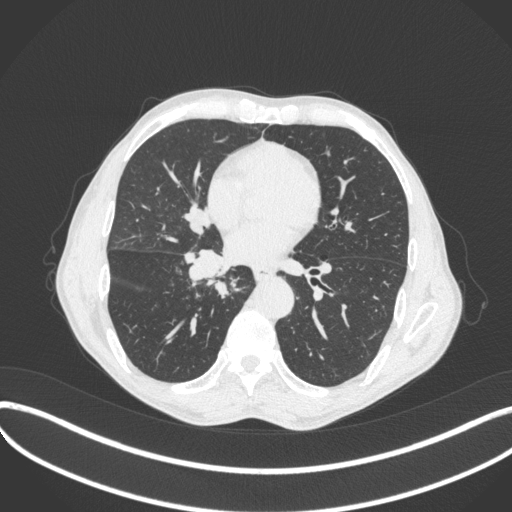
Chest CT, one axial slice. Position 197 of 481 along the scan axis. Reconstruction kernel B31f. 120 kVp. Lung window (W 1500 / L -600 HU). 1 mm slice thickness. 512 × 512 image matrix, field of view 400 × 400 mm. Male patient, age 65 years. Case-level facts recorded for this patient, not image findings: clinical TNM (as recorded): T2a N0 M0; histopathological grade: G2.
Structures marked on this image (rectangle marked by the reading radiologist):
- lung tumour (recorded histology: squamous cell carcinoma): box from (x=180, y=246) to (x=235, y=285) px